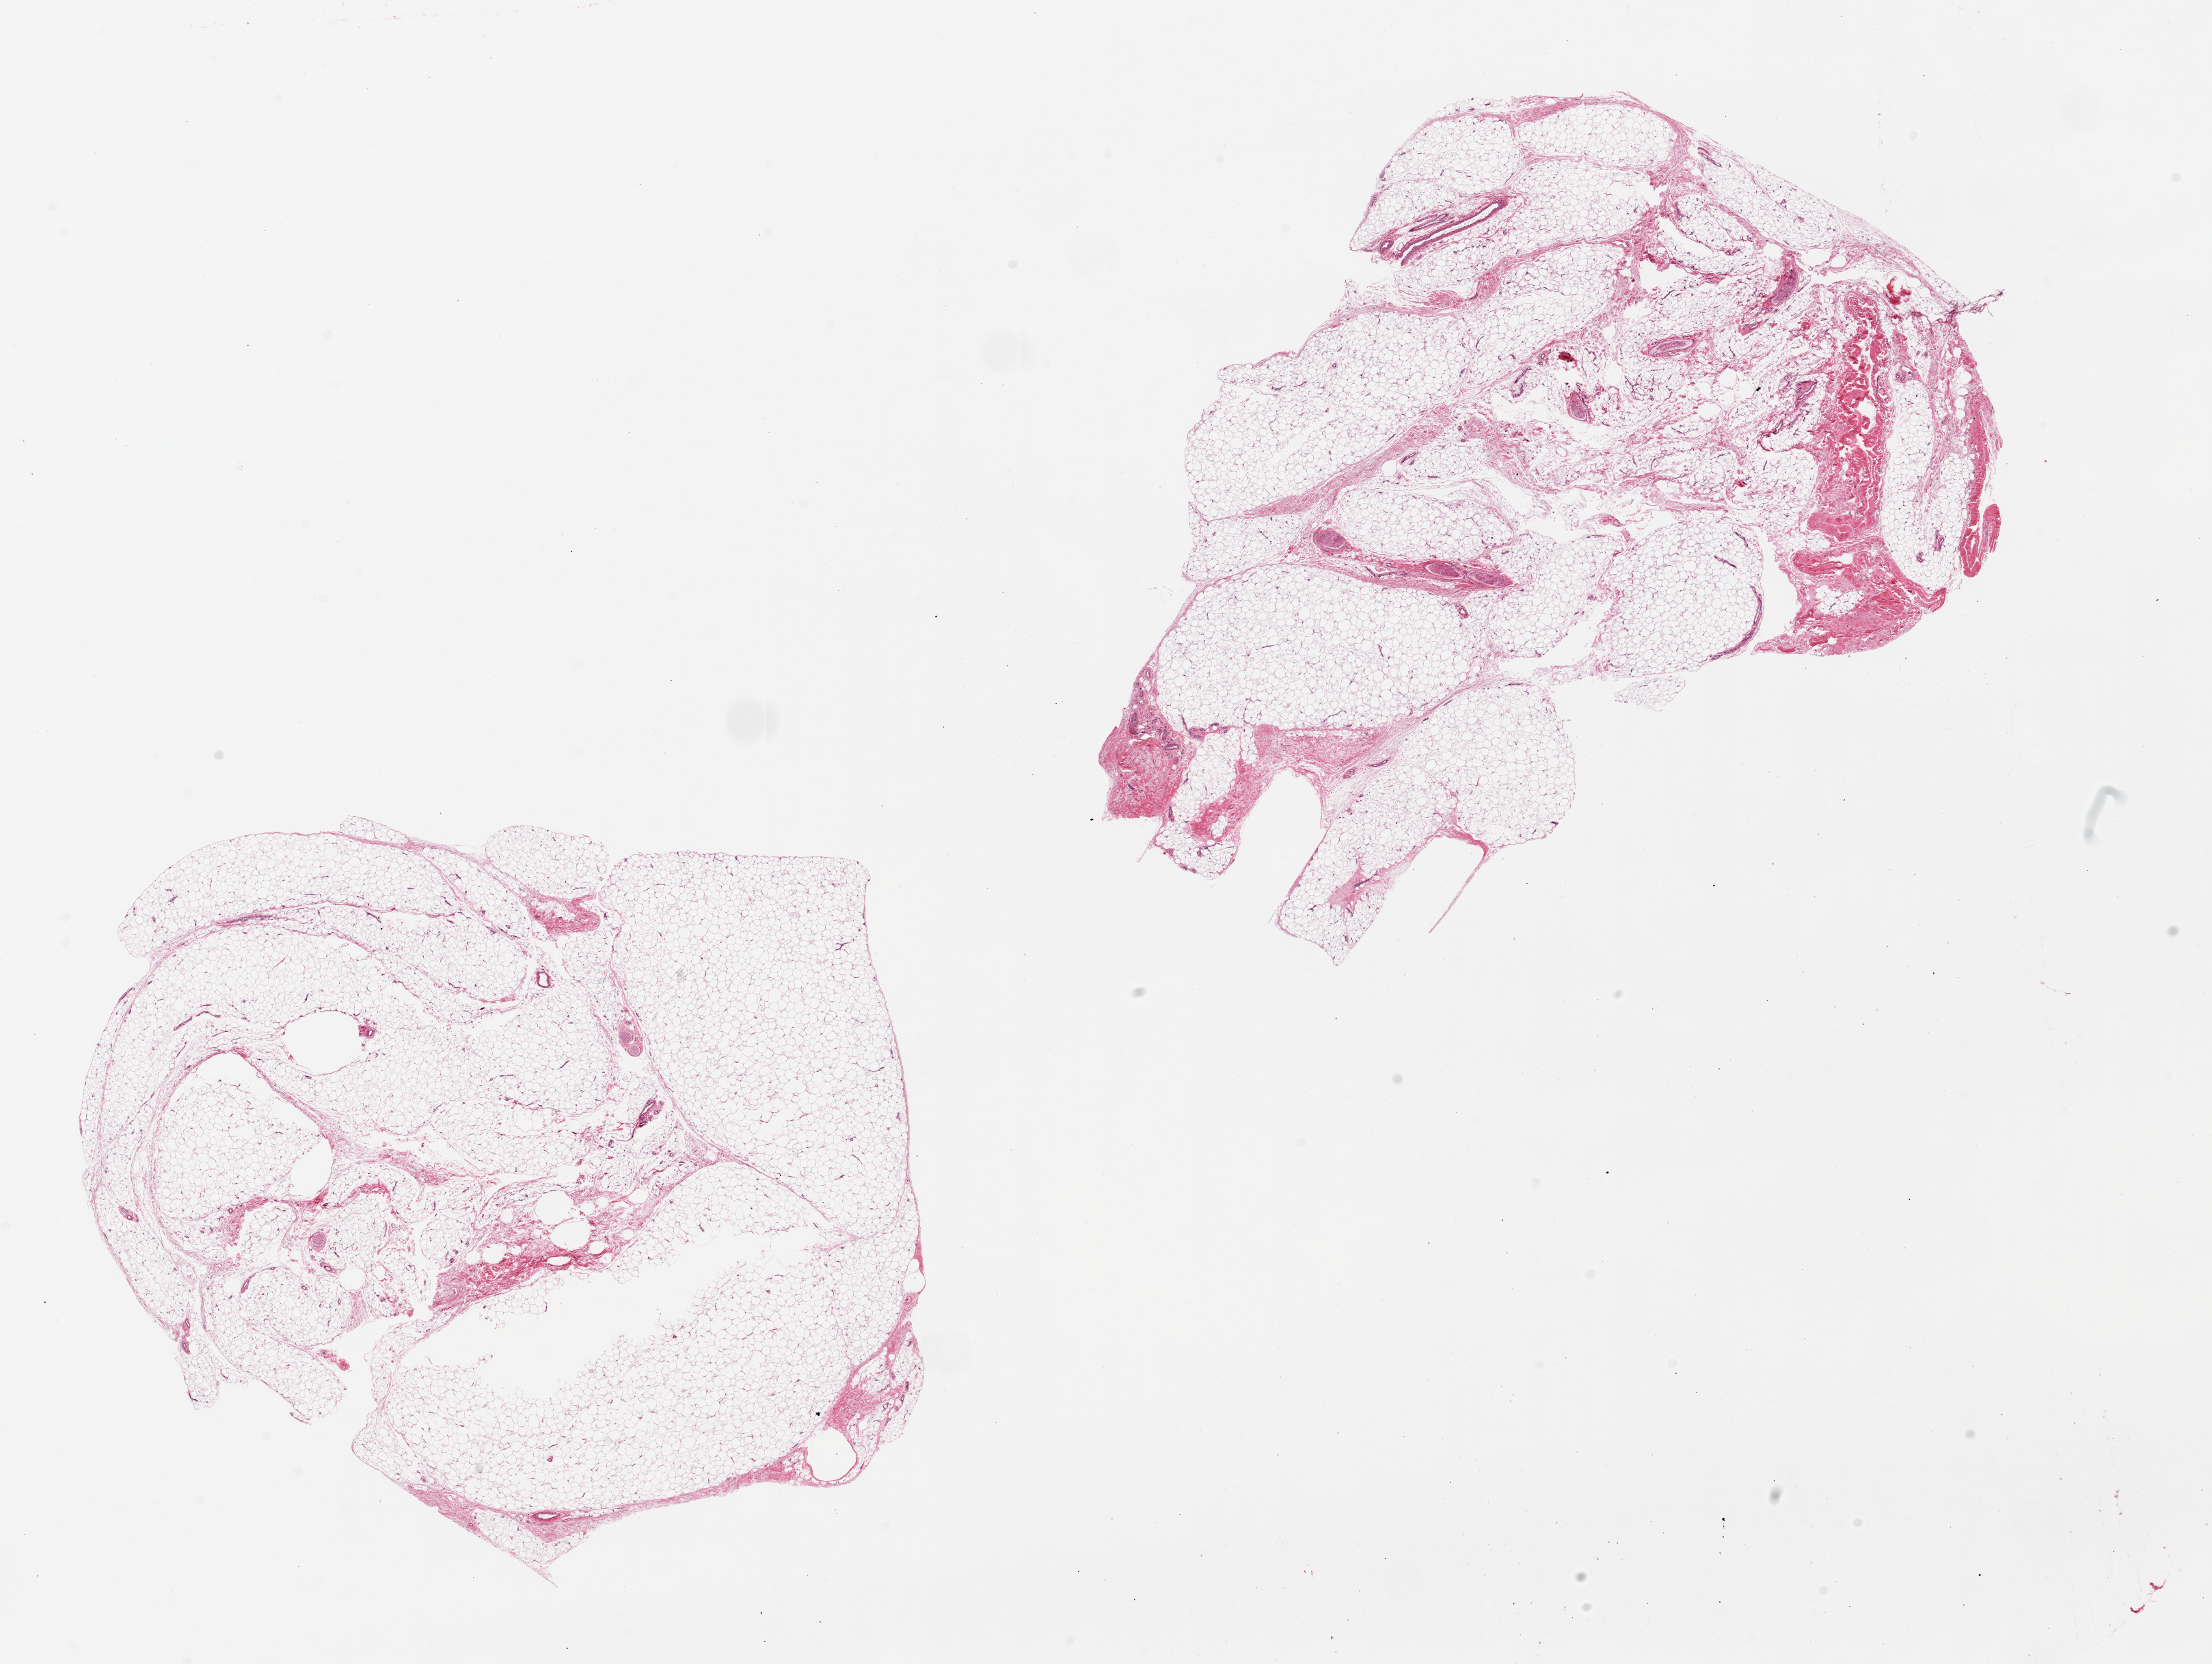
Digitized hematoxylin and eosin (H&E)-stained section, brightfield — whole scanned area (about 25.6 x 19.3 mm, acquisition: 20x scan) shown as a low-resolution overview; PAXgene-fixed paraffin-embedded (PFPE) section; target tissue: adipose tissue; donor tissue sample. Female donor.
Review note (as recorded): 2 pieces, 11x10 & 12x8mm; ~10% fibrous tissue.